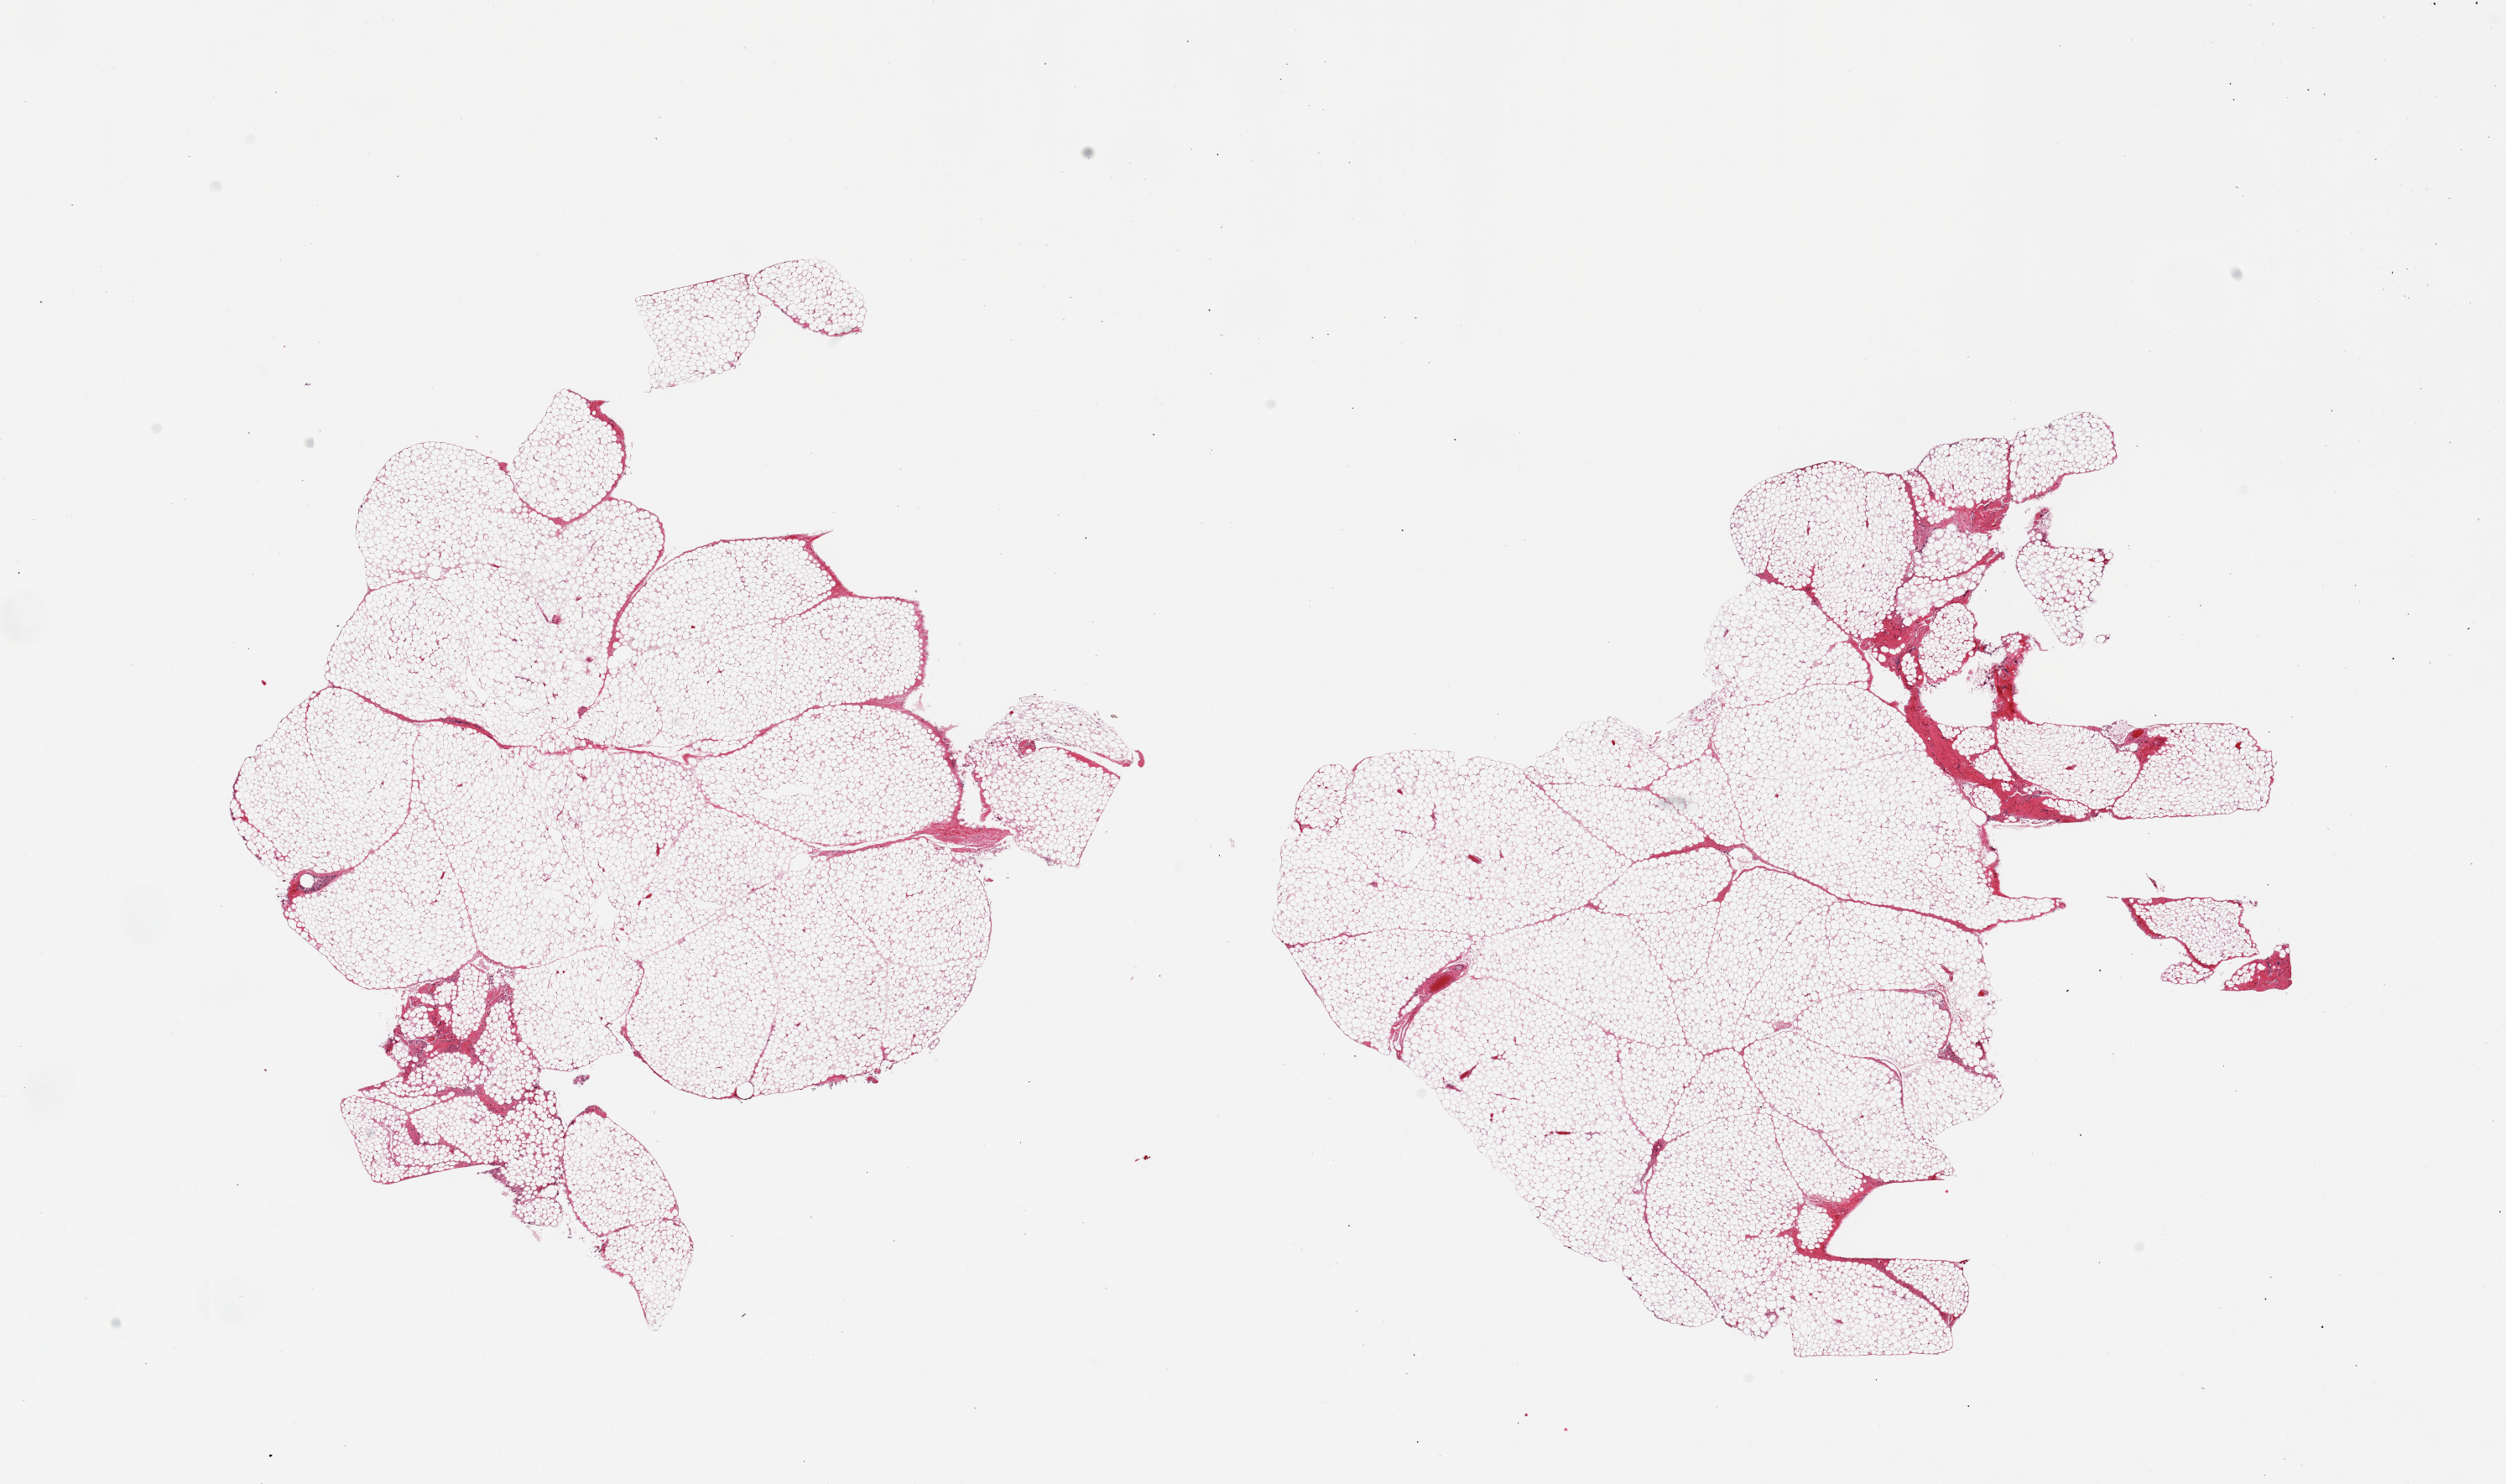
Digitized hematoxylin and eosin (H&E)-stained section, shown as a low-resolution overview of the whole scanned area (about 23.6 x 14.0 mm); PAXgene-fixed, paraffin-embedded tissue; target tissue: omentum; tissue donor sample. Donor: female.
- review note (as recorded): 2 pieces